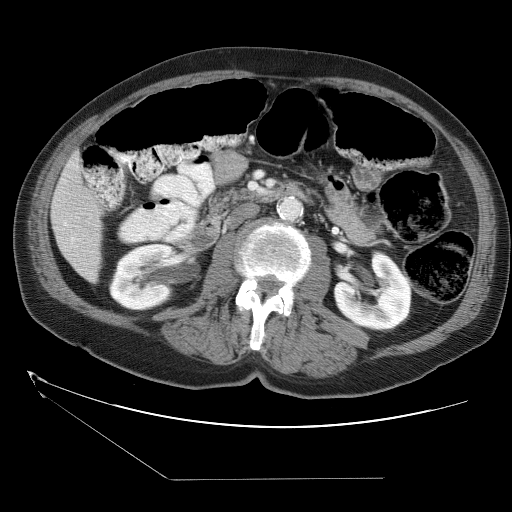
Contrast-enhanced abdominal CT (liver protocol), one axial slice; position 7 of 38 along the scan axis; reconstruction kernel STANDARD; 120 kVp; soft-tissue window (W 400 / L 40 HU); 5 mm slice thickness; 512 × 512 image matrix, field of view 400 × 400 mm. Case-level facts recorded for this patient, not image findings: diagnosis: hepatocellular carcinoma (patient treated with transarterial chemoembolisation; whether this scan precedes or follows treatment is not stated here); TNM stage (as recorded): Stage-II; Child-Pugh class: A; tumour nodularity: multinodular; tumour size: 0.8 cm.
Structures marked on this image (semi-automatic segmentation, software-assisted and operator-edited):
- liver parenchyma outside the tumour (the mass and vessels are separate outlines, so this box may not span the whole liver): bounding box <50,150,104,282> (left, top, right, bottom; pixels)
- liver vessels: <64,223,67,226>